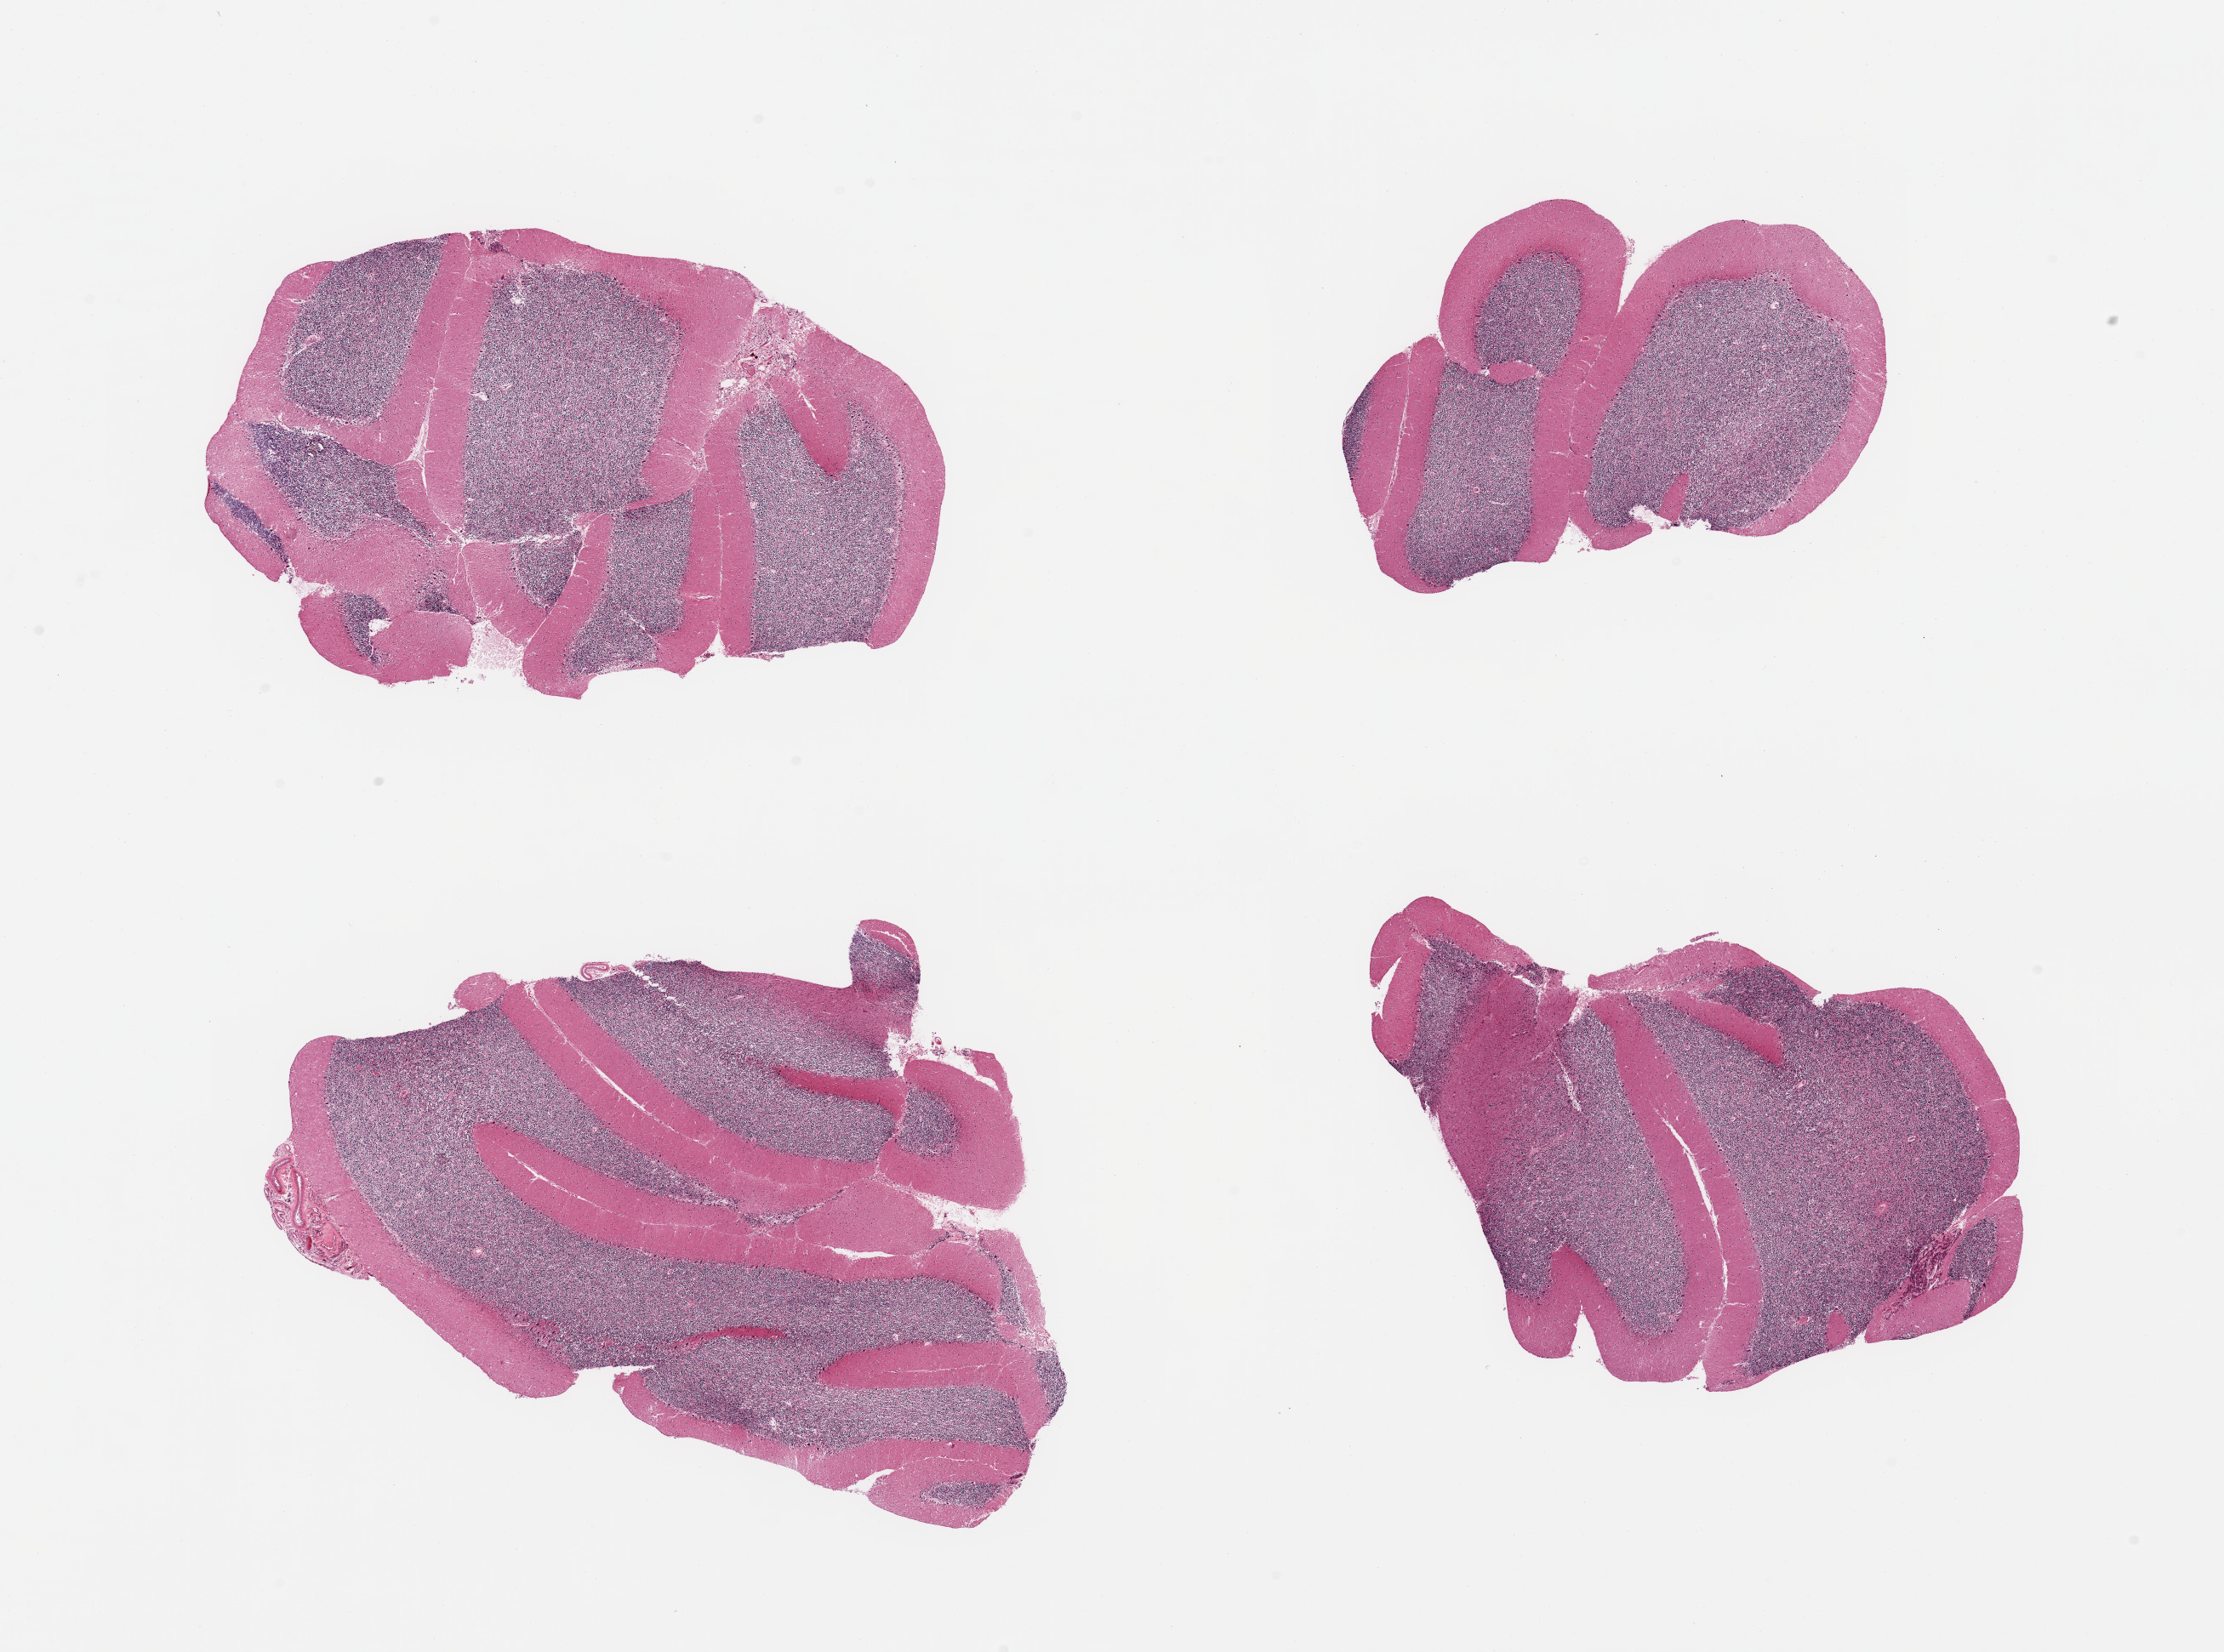
Hematoxylin and eosin (H&E) whole-slide image, brightfield, a low-resolution overview of the entire scanned area, about 20.7 x 15.4 mm. PAXgene-fixed paraffin-embedded (PFPE) section. Sampled site (target tissue): cerebellum. Tissue donor sample. Male donor.
- pathologist's review note for this sample: 4 pieces